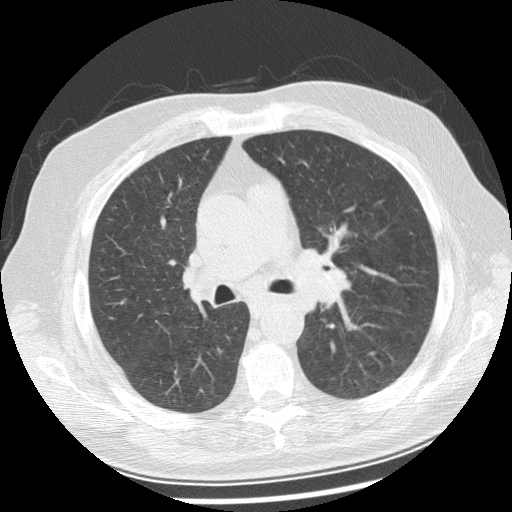
Chest CT (low-dose screening protocol), one axial image. Baseline screening round. Lung window (W 1500 / L -600 HU). 512 × 512 image matrix, field of view 360 × 360 mm. Male participant, aged 70 years at enrolment. Current smoker at enrolment.
- Expert-annotated lung lesion, bounding box (x1, y1, x2, y2) in pixels: (280, 242, 362, 308).
- Screening reader's record for this exam: no non-calcified nodule ≥4 mm recorded.
- Official screen result: positive, change unspecified: nodule(s) >= 4 mm or enlarging nodule(s), mass(es), or other non-specific abnormalities suspicious for lung cancer.
- Participant outcome: lung cancer diagnosed 29 days after this screen — squamous cell carcinoma, keratinizing, NOS, left main stem bronchus, moderately differentiated (G2), stage IIIB (AJCC 6th edition), 40 mm at pathology.